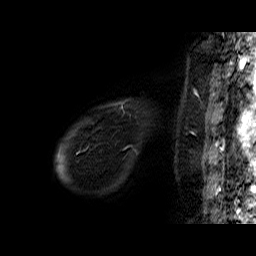
Breast MRI (dynamic contrast-enhanced), one sagittal slice; position 4 of 60 along the scan axis; dynamic contrast-enhanced series, time point 2 of 6 at this slice position (early post-contrast); 1.5 T; TE 6.4 ms, TR 32.9 ms; 4 mm slice thickness; 256 × 256 image matrix, field of view 200 × 200 mm. Female patient. From the clinical record (not read from this slice): setting: breast cancer imaged before/during neoadjuvant chemotherapy; receptor status: HER2-positive.
Annotated regions visible in this slice (semi-automatically segmented with operator editing):
- analysis volume of interest (the breast-tissue region the enhancement analysis was run in; not a lesion): bounding box <71,98,151,146> (left, top, right, bottom; pixels)
- tumour enhancement mask (voxels above the 100 % enhancement threshold inside the analysis volume of interest): <103,100,128,108>